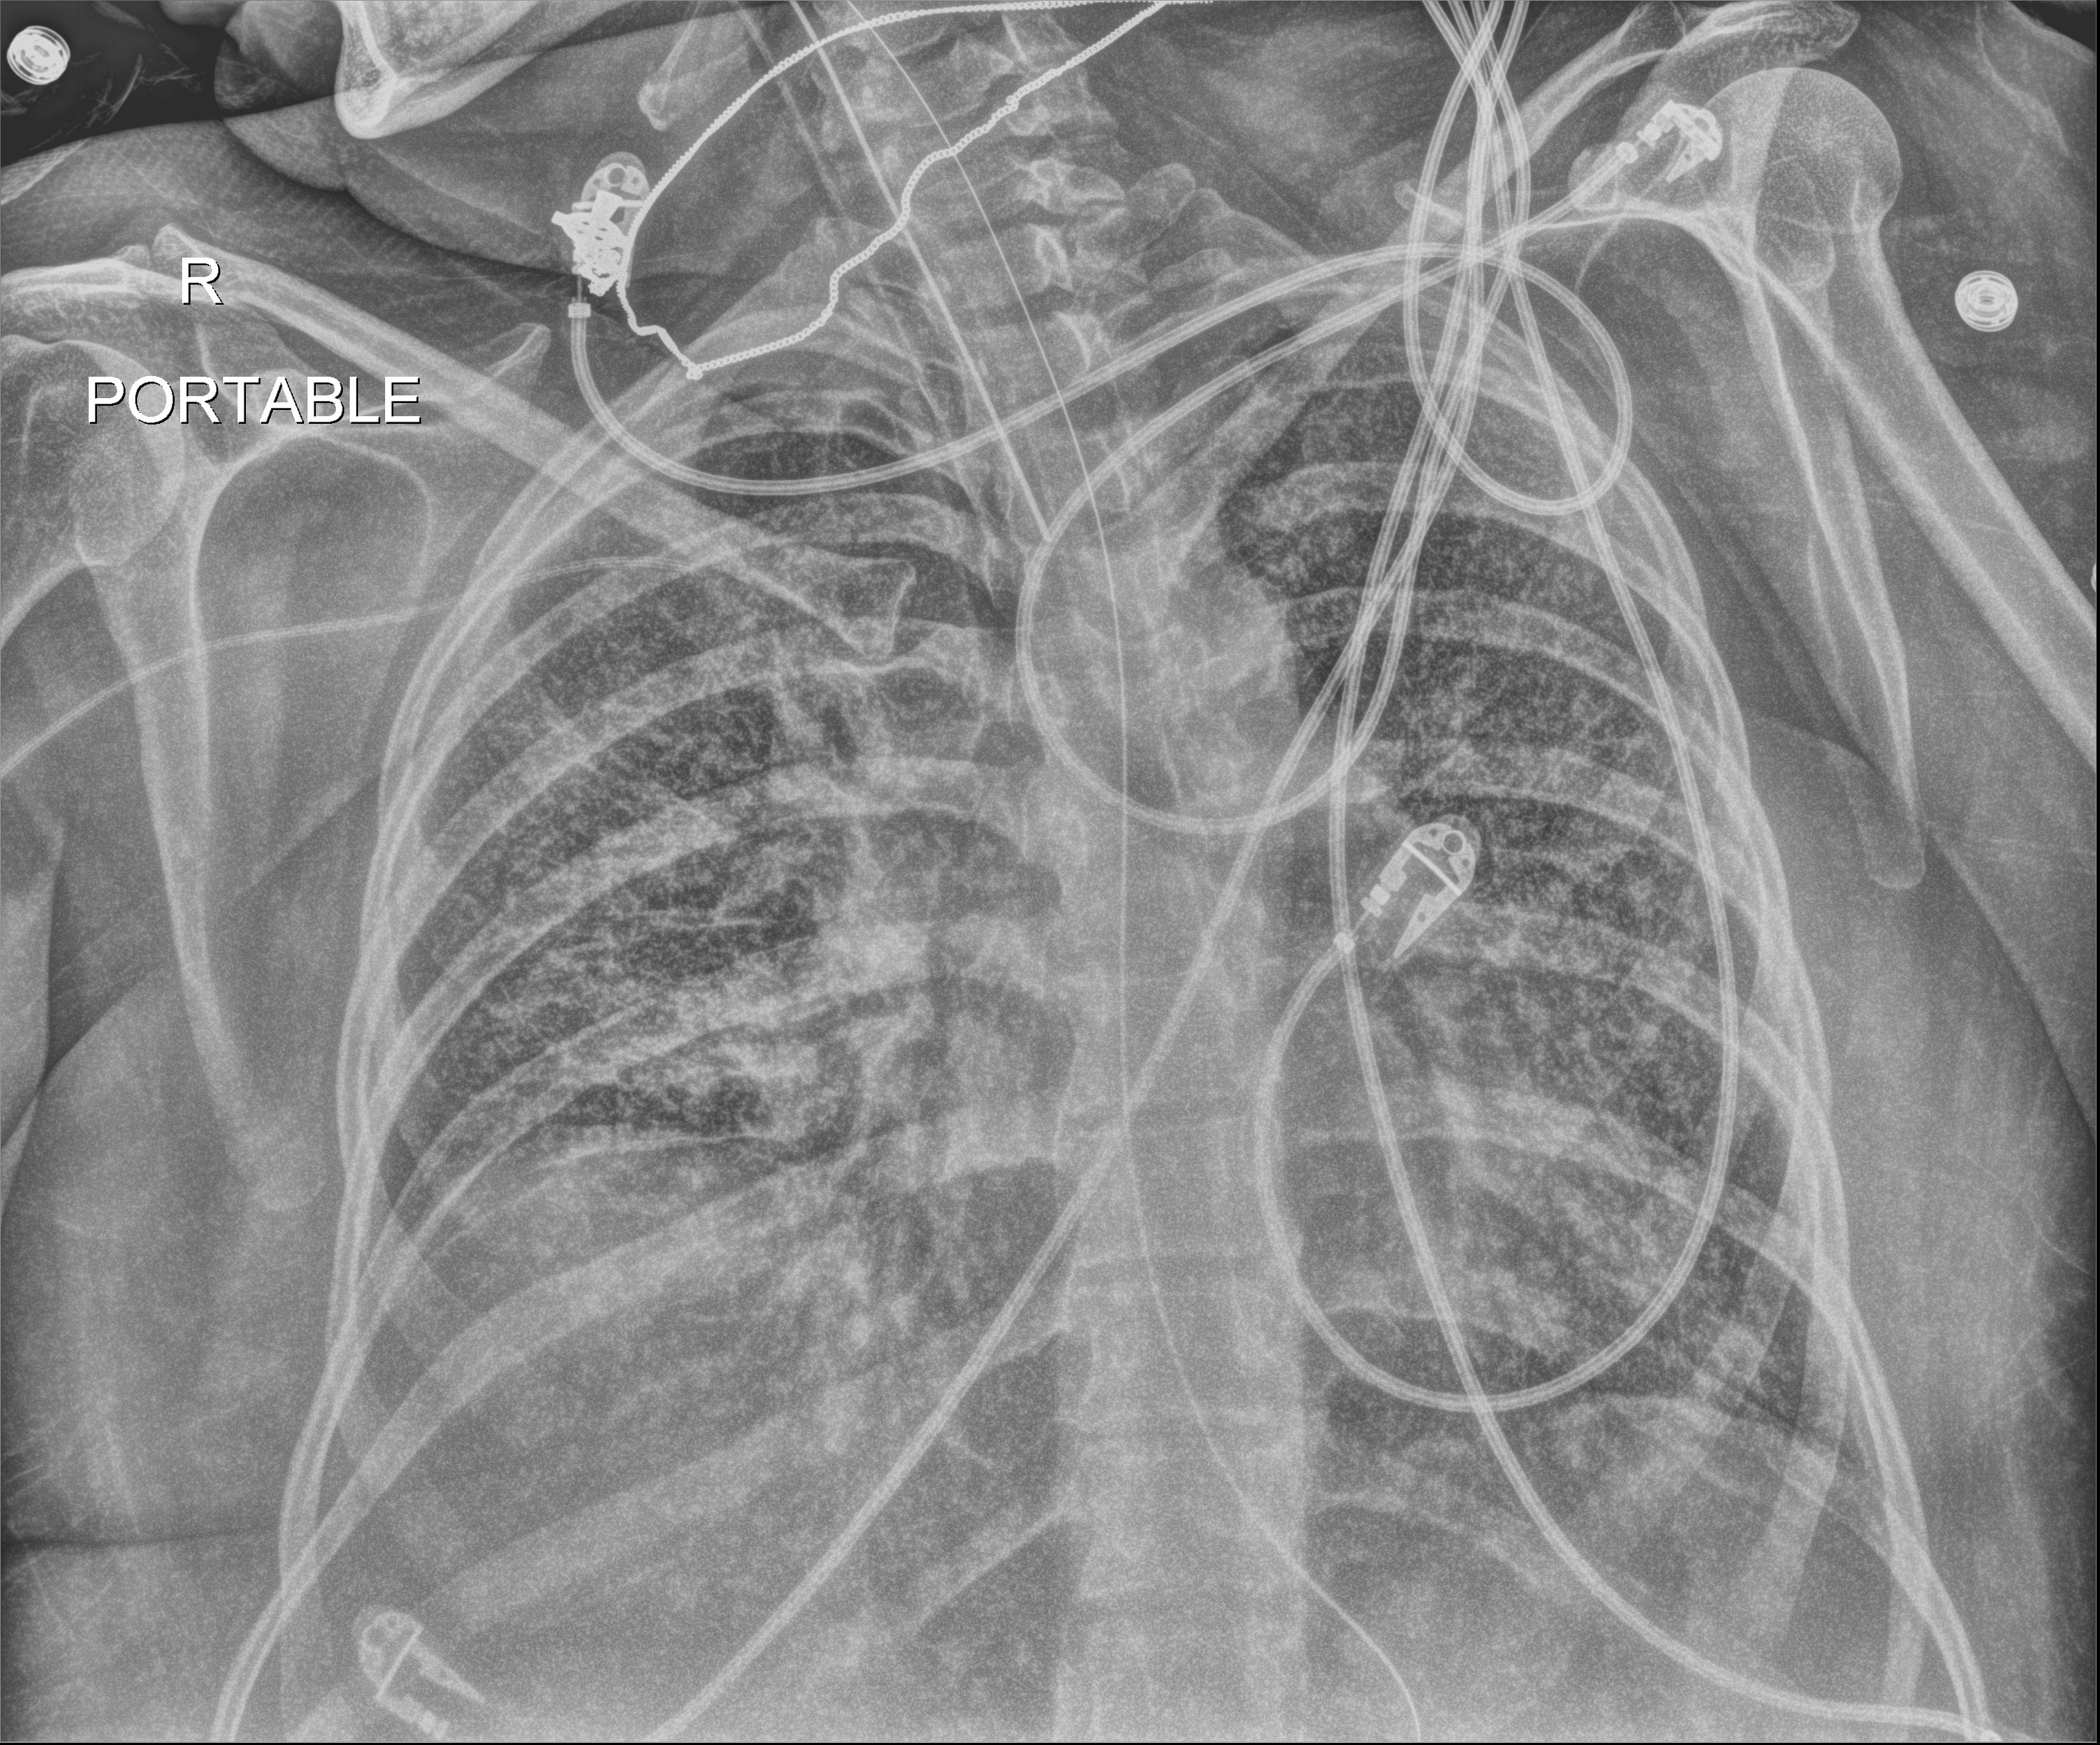
Chest radiograph (digital radiography), anteroposterior (AP) projection. Female patient hospitalised with COVID-19, age 18–59 years.
From the hospital-stay record, not from the radiograph (when in the stay this image was taken is not recorded): mechanically ventilated during this hospital stay: yes; admitted to intensive care during this hospital stay: yes; diabetes (admission record): no.